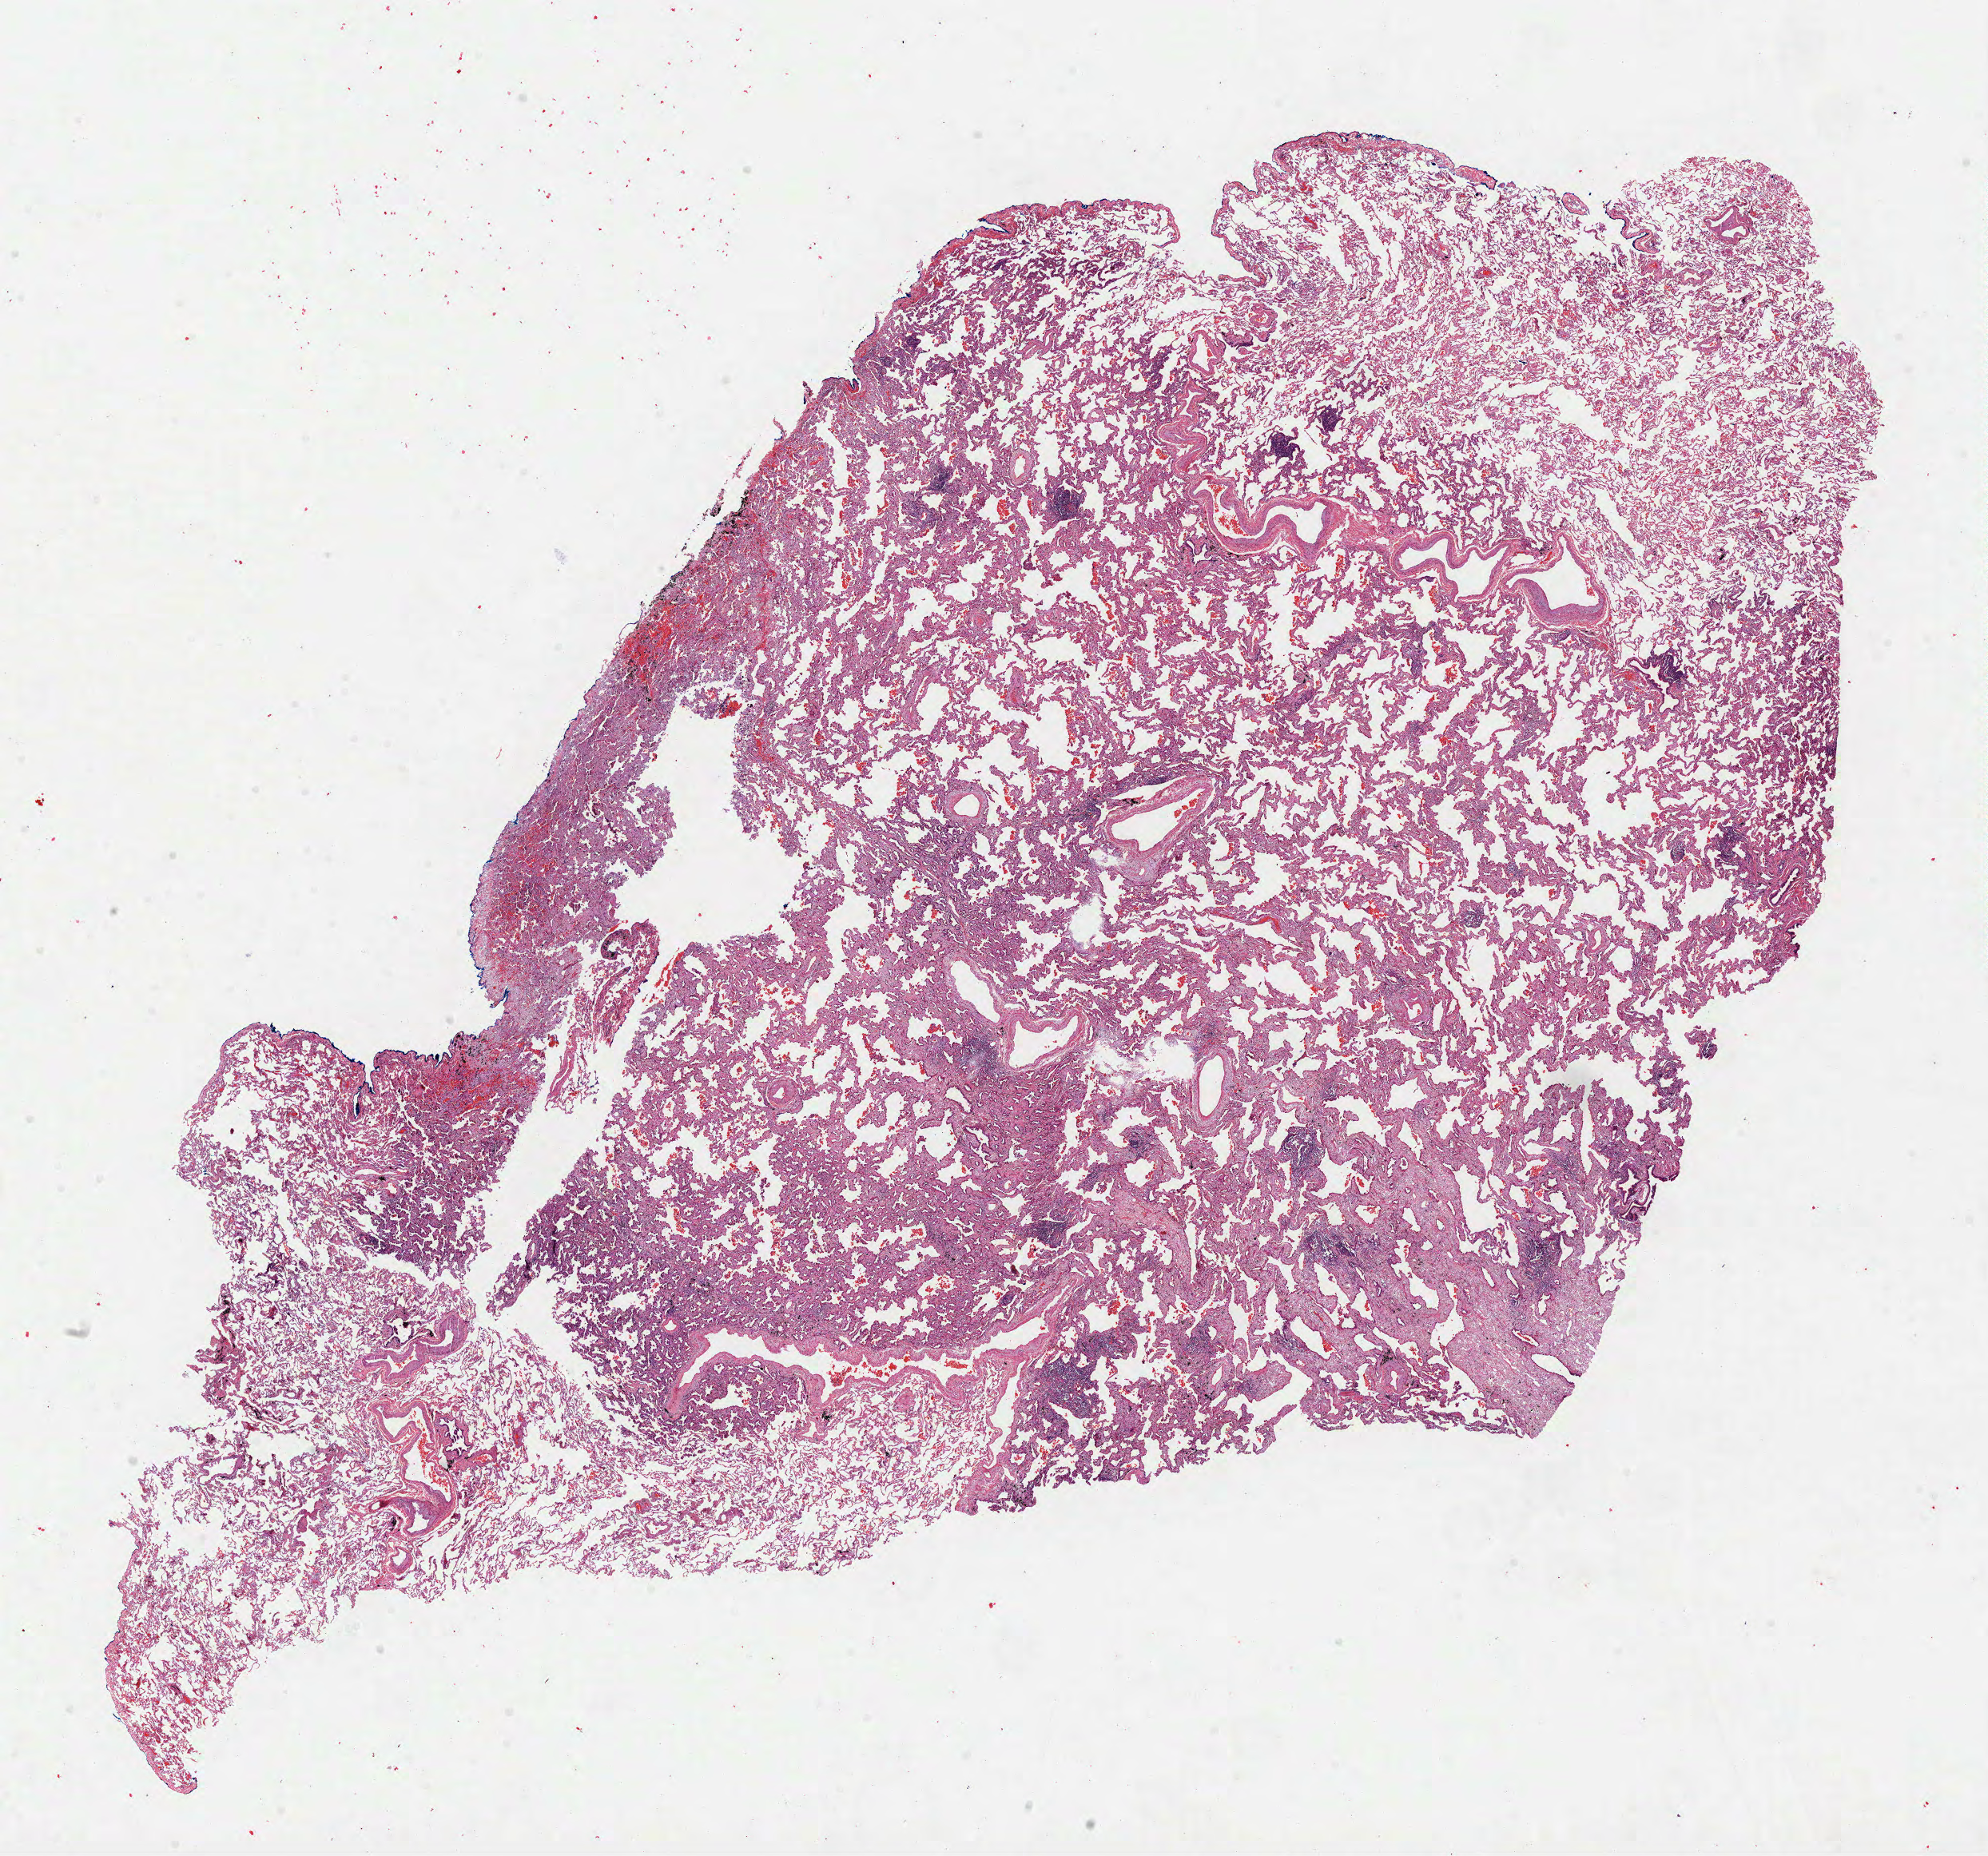
Digitized Hematoxylin and eosin (H&E) stained tissue section (whole slide) — a low-resolution overview of the entire scanned area, about 20.1 x 18.7 mm (slide scanned at 40x). FFPE section. Sample: primary tumour, lung. Female patient; age at initial diagnosis 76 years.
Diagnosis: Acinar cell carcinoma (upper lobe, lung). AJCC pathologic stage: IA (6th edition).